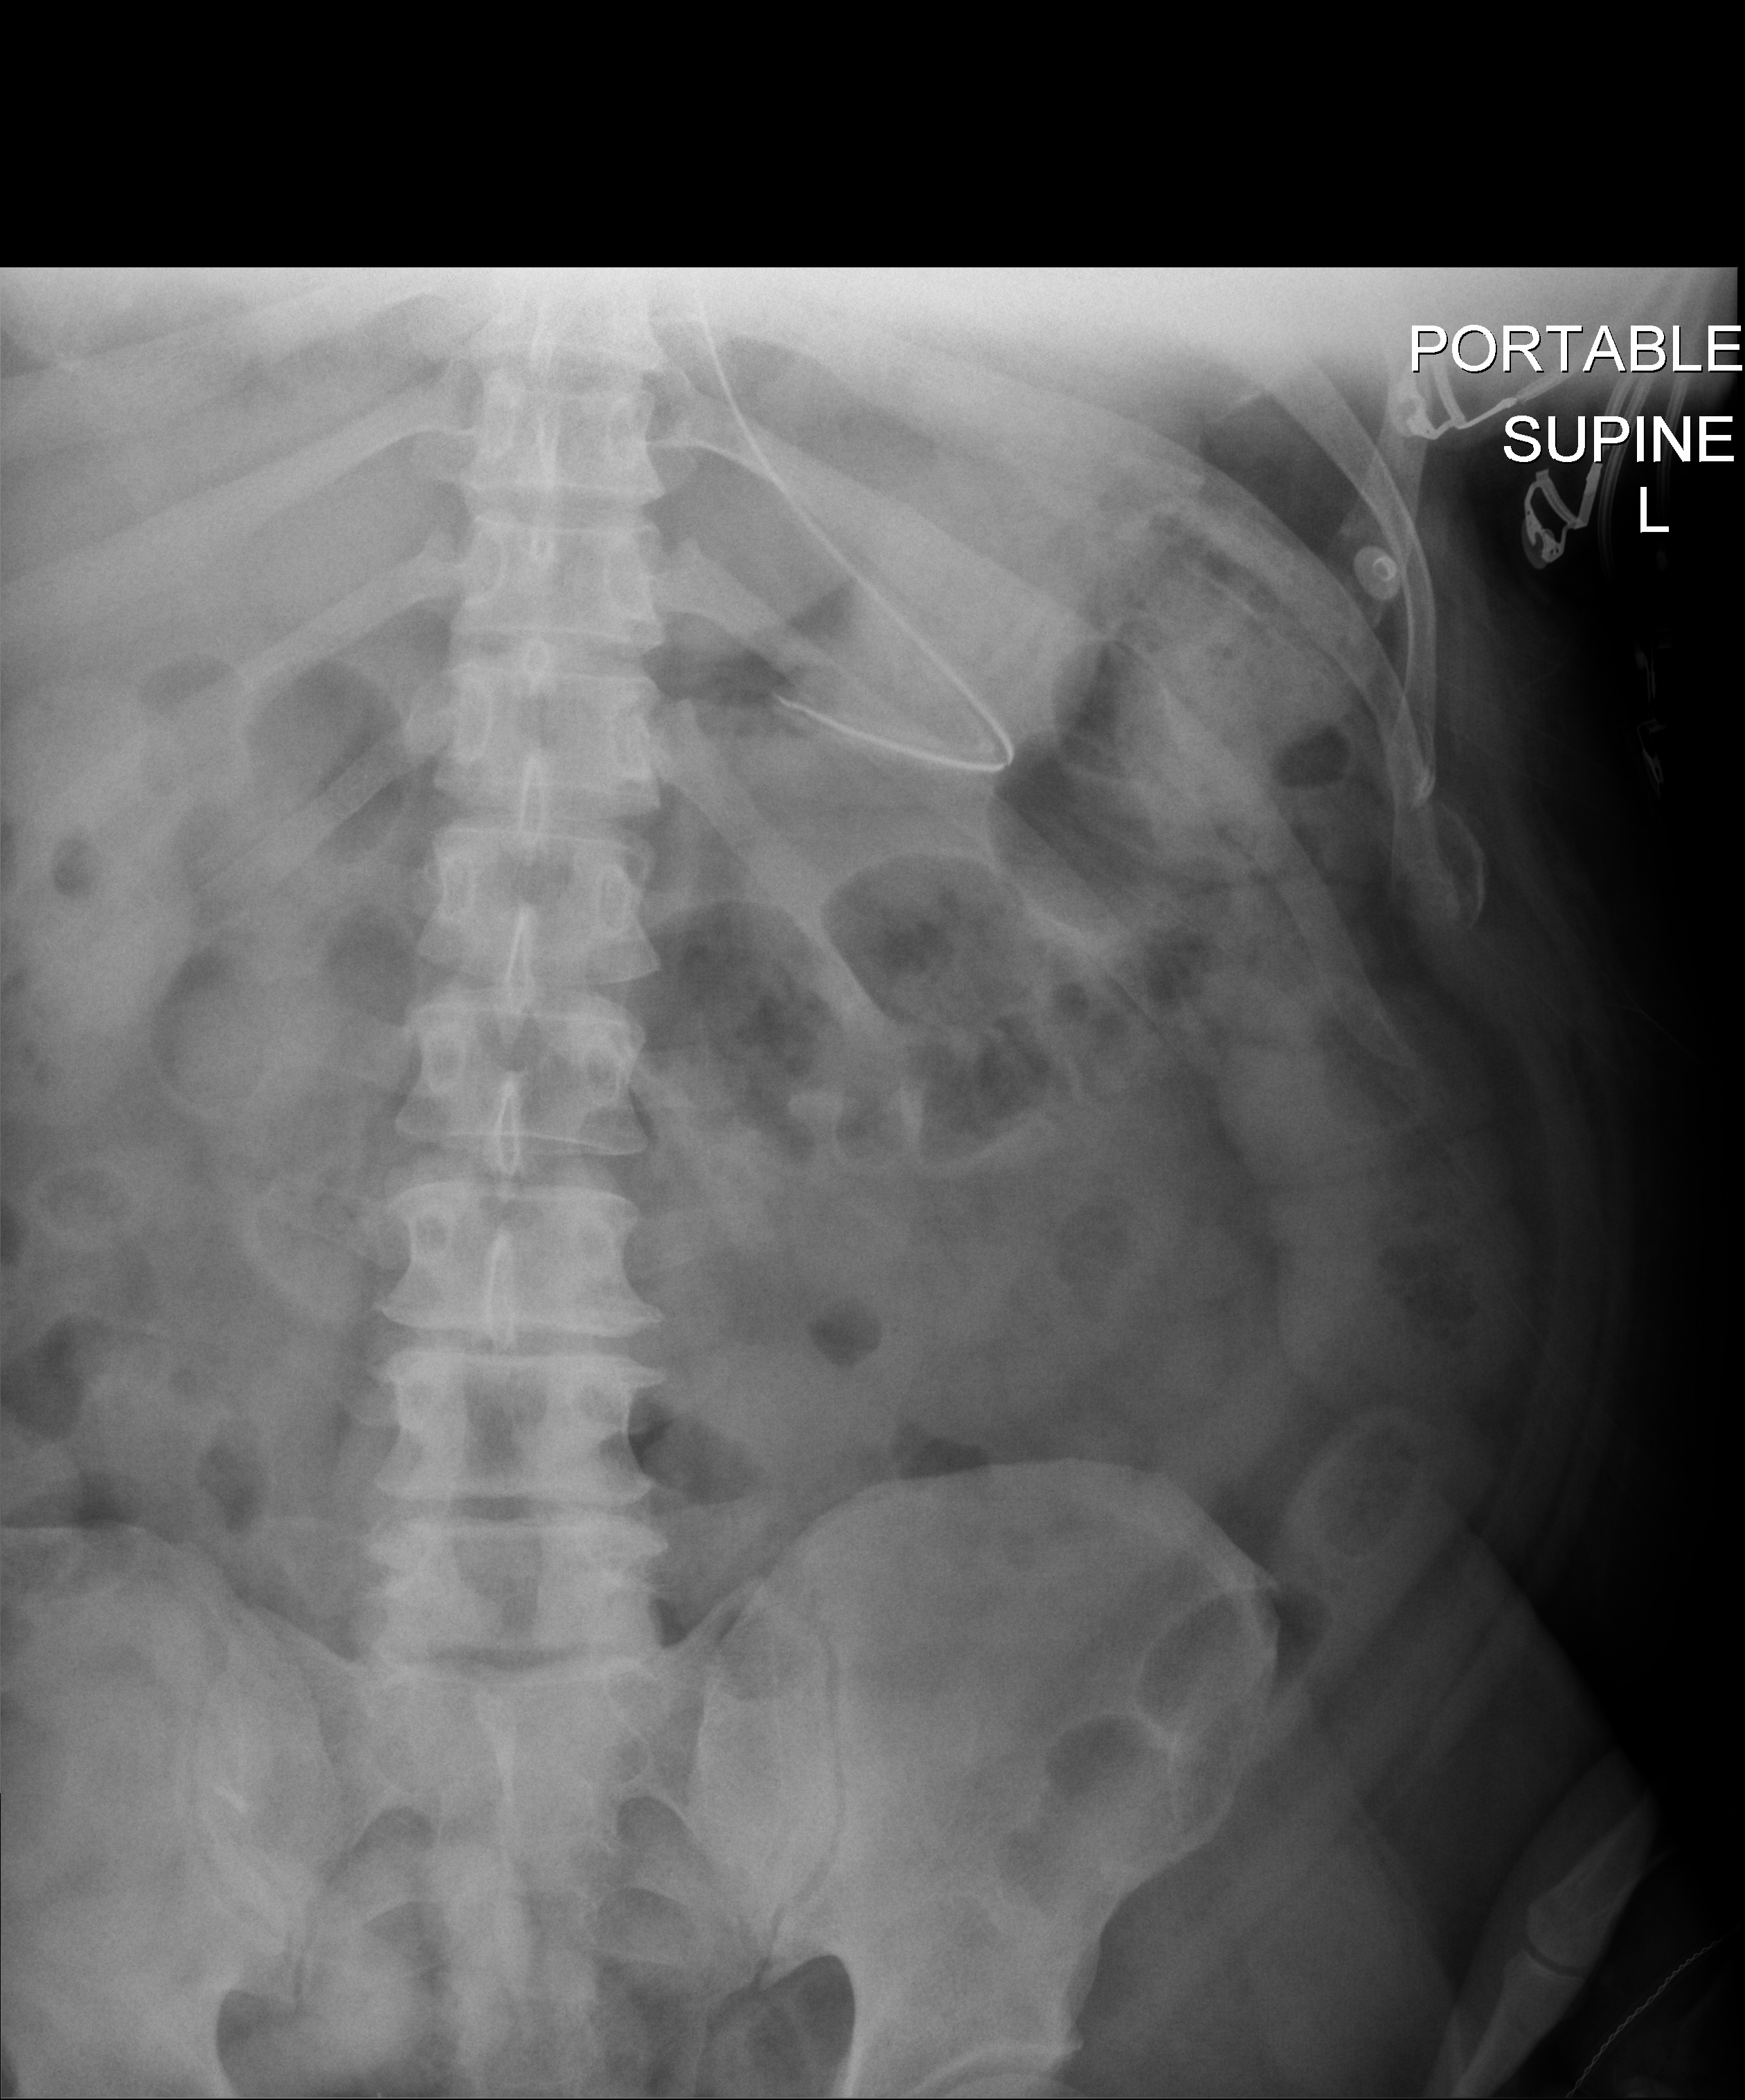
Portable abdomen radiograph, anteroposterior (AP) projection. Male patient hospitalised with COVID-19, age 18–59 years.
Admission-level facts for this patient (not findings on this image; timing relative to this image not recorded): other chronic lung disease (admission record): no.